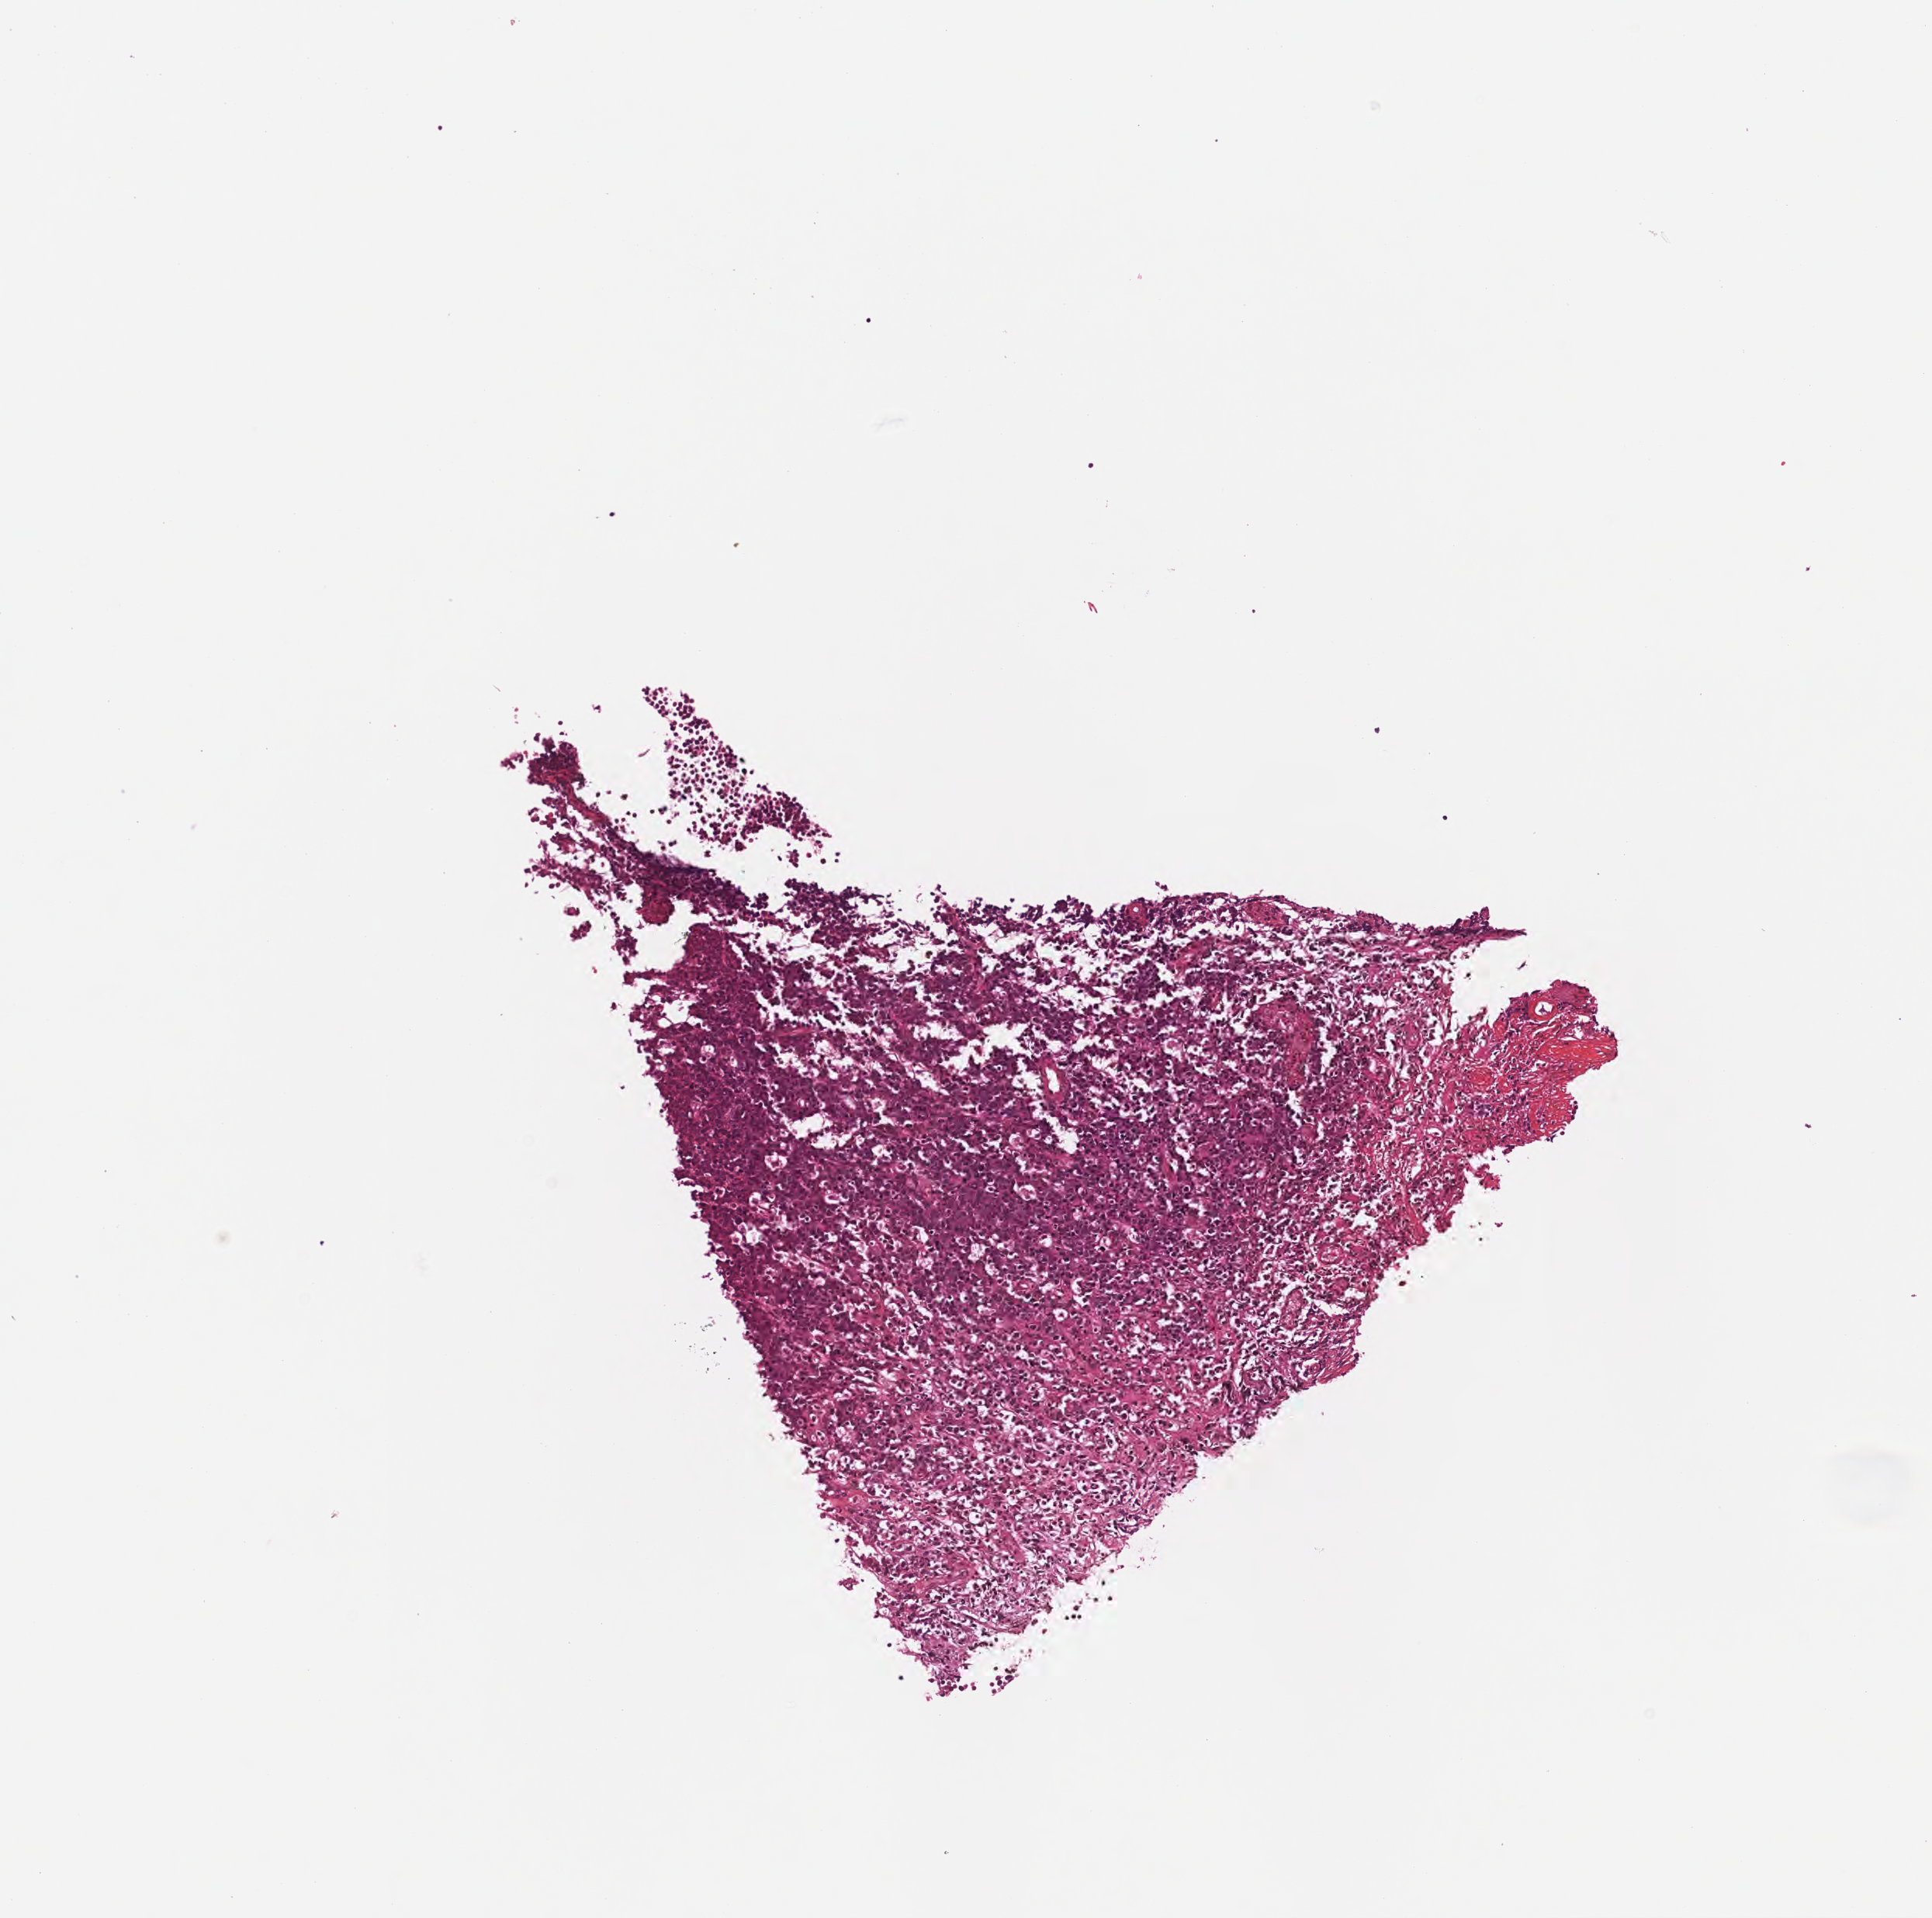
Whole-slide image, haematoxylin and eosin stain, shown as a low-resolution overview of the whole scanned area (about 2.5 x 2.5 mm). FFPE section. Specimen: primary tumor. Patient: male, age at initial diagnosis 2 years. Slide review estimates, as recorded: tumor cells 85%, tumor nuclei 90%, stromal cells 10%, necrosis 5%, normal cells 0%. Infiltration values recorded for this section: lymphocyte infiltration 75%, monocyte infiltration 15%, neutrophil infiltration 5%.
Ann Arbor stage (patient): Stage III. Histologic diagnosis: Burkitt lymphoma, NOS.